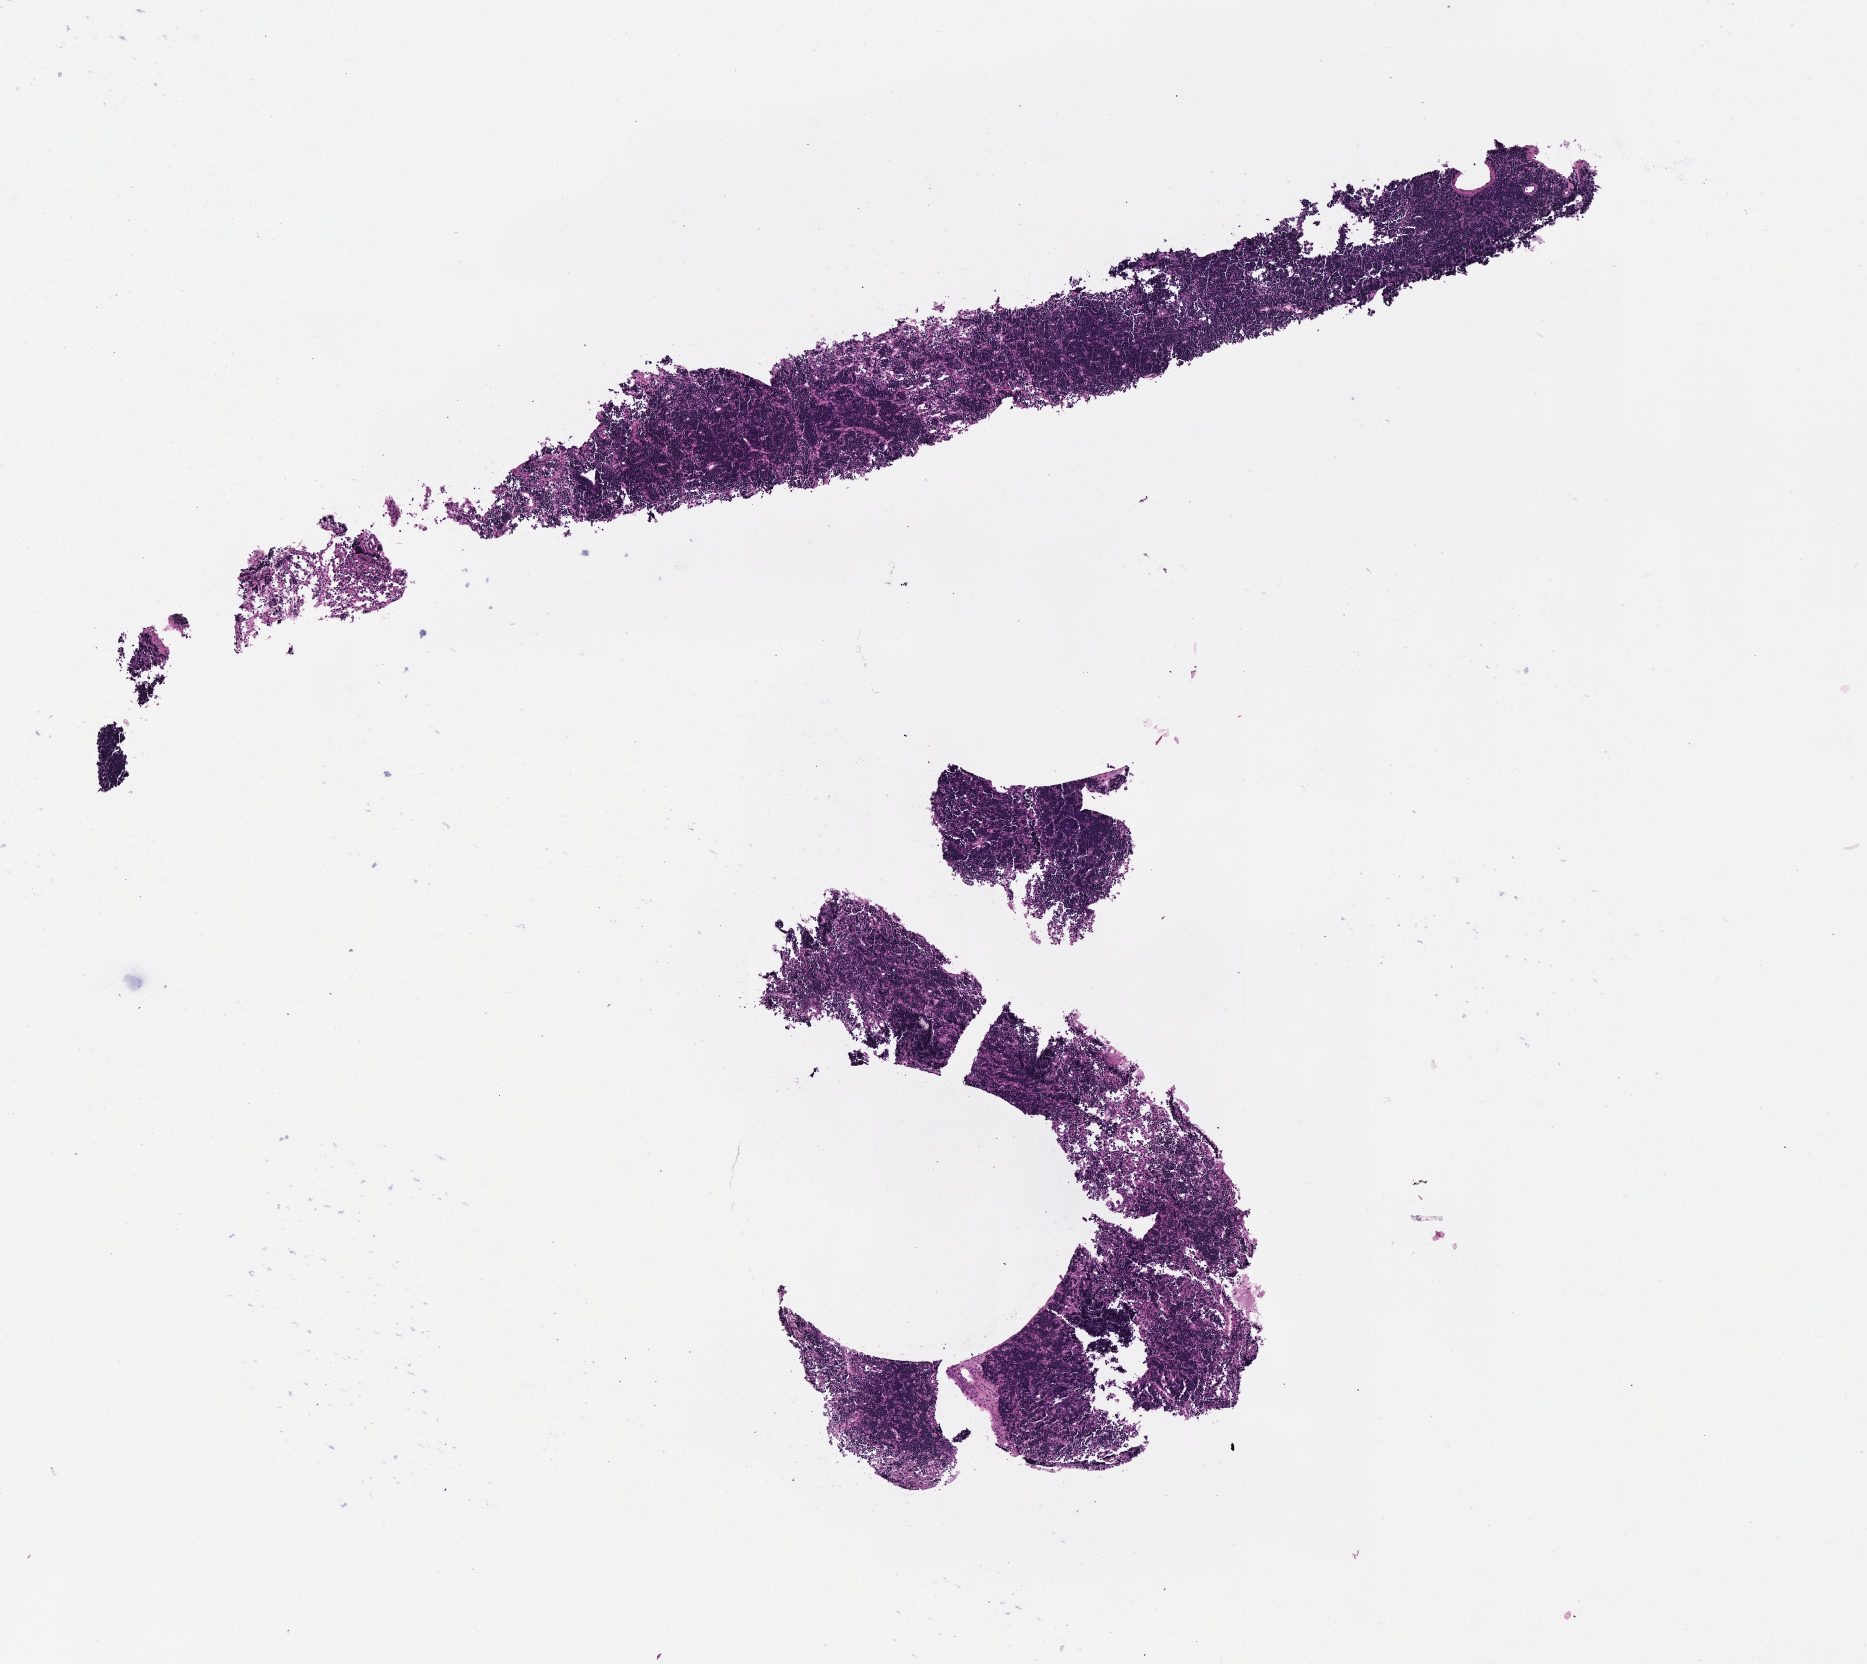
Digitized haematoxylin and eosin-stained section — a low-resolution overview of the entire scanned area, about 7.5 x 6.7 mm. Specimen: tumor tissue. Anatomic site: ovary. Patient: female, 10 years old.
- histologic diagnosis: Burkitt lymphoma, NOS